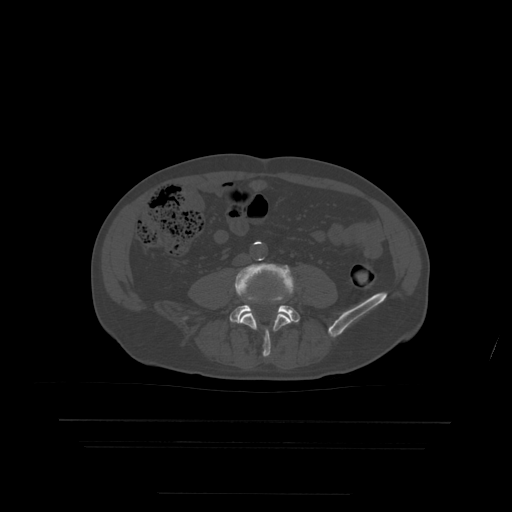
CT including the spine, one axial slice. Position 86 of 522 along the scan axis. Bone window (W 1800 / L 400 HU). 512 × 512 image matrix, field of view 436 × 436 mm. Patient age 68 years. From the clinical record (not read from this slice): primary cancer: urothelial.
Outlined on this slice (semi-automatic segmentation, software-assisted and operator-edited):
- L4 vertebra: box from (x=235, y=263) to (x=295, y=357) px
- L5 vertebra: (x=230, y=298)–(x=301, y=324)